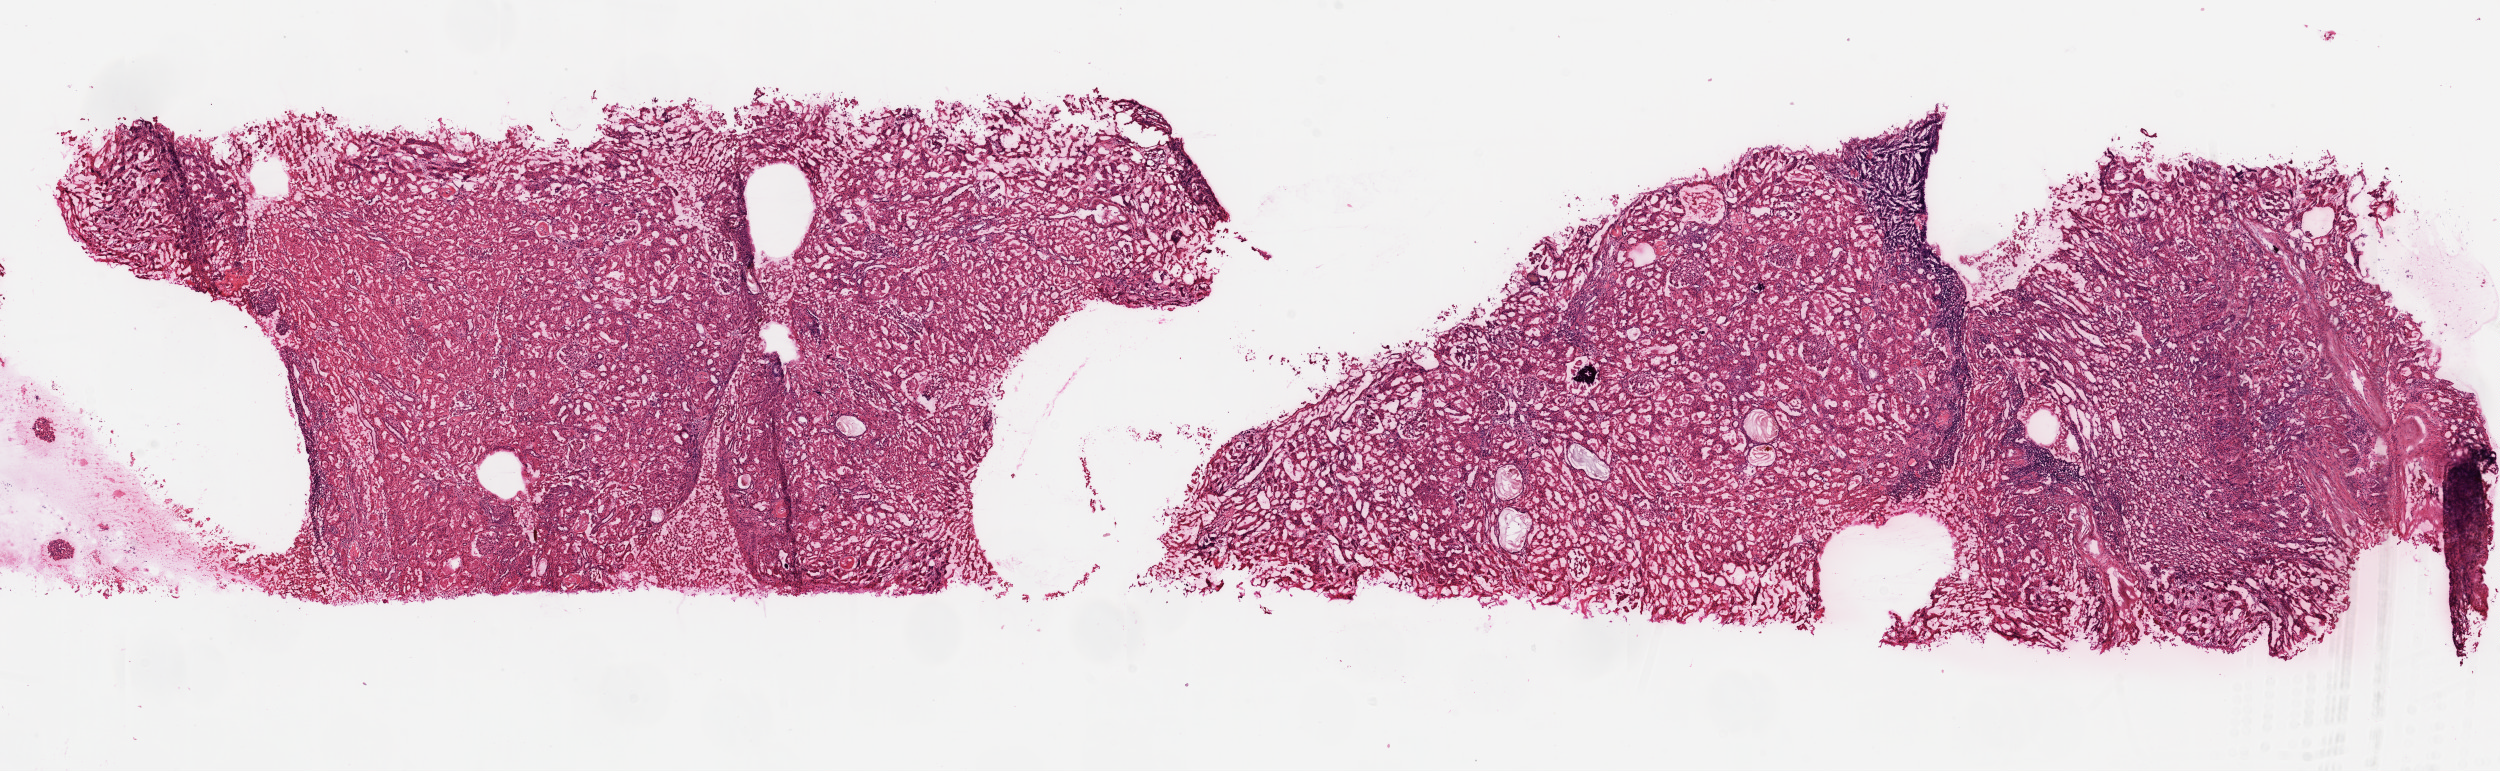
Digitized H&E tissue section (whole slide), a low-resolution overview of the entire scanned area, about 20.1 x 6.2 mm, frozen section, kidney, solid tissue normal (non-tumour tissue) sample. Female, age 72 years at initial diagnosis.
This section: solid tissue normal sample (biorepository sample class). Patient diagnosis: Clear cell adenocarcinoma, NOS.